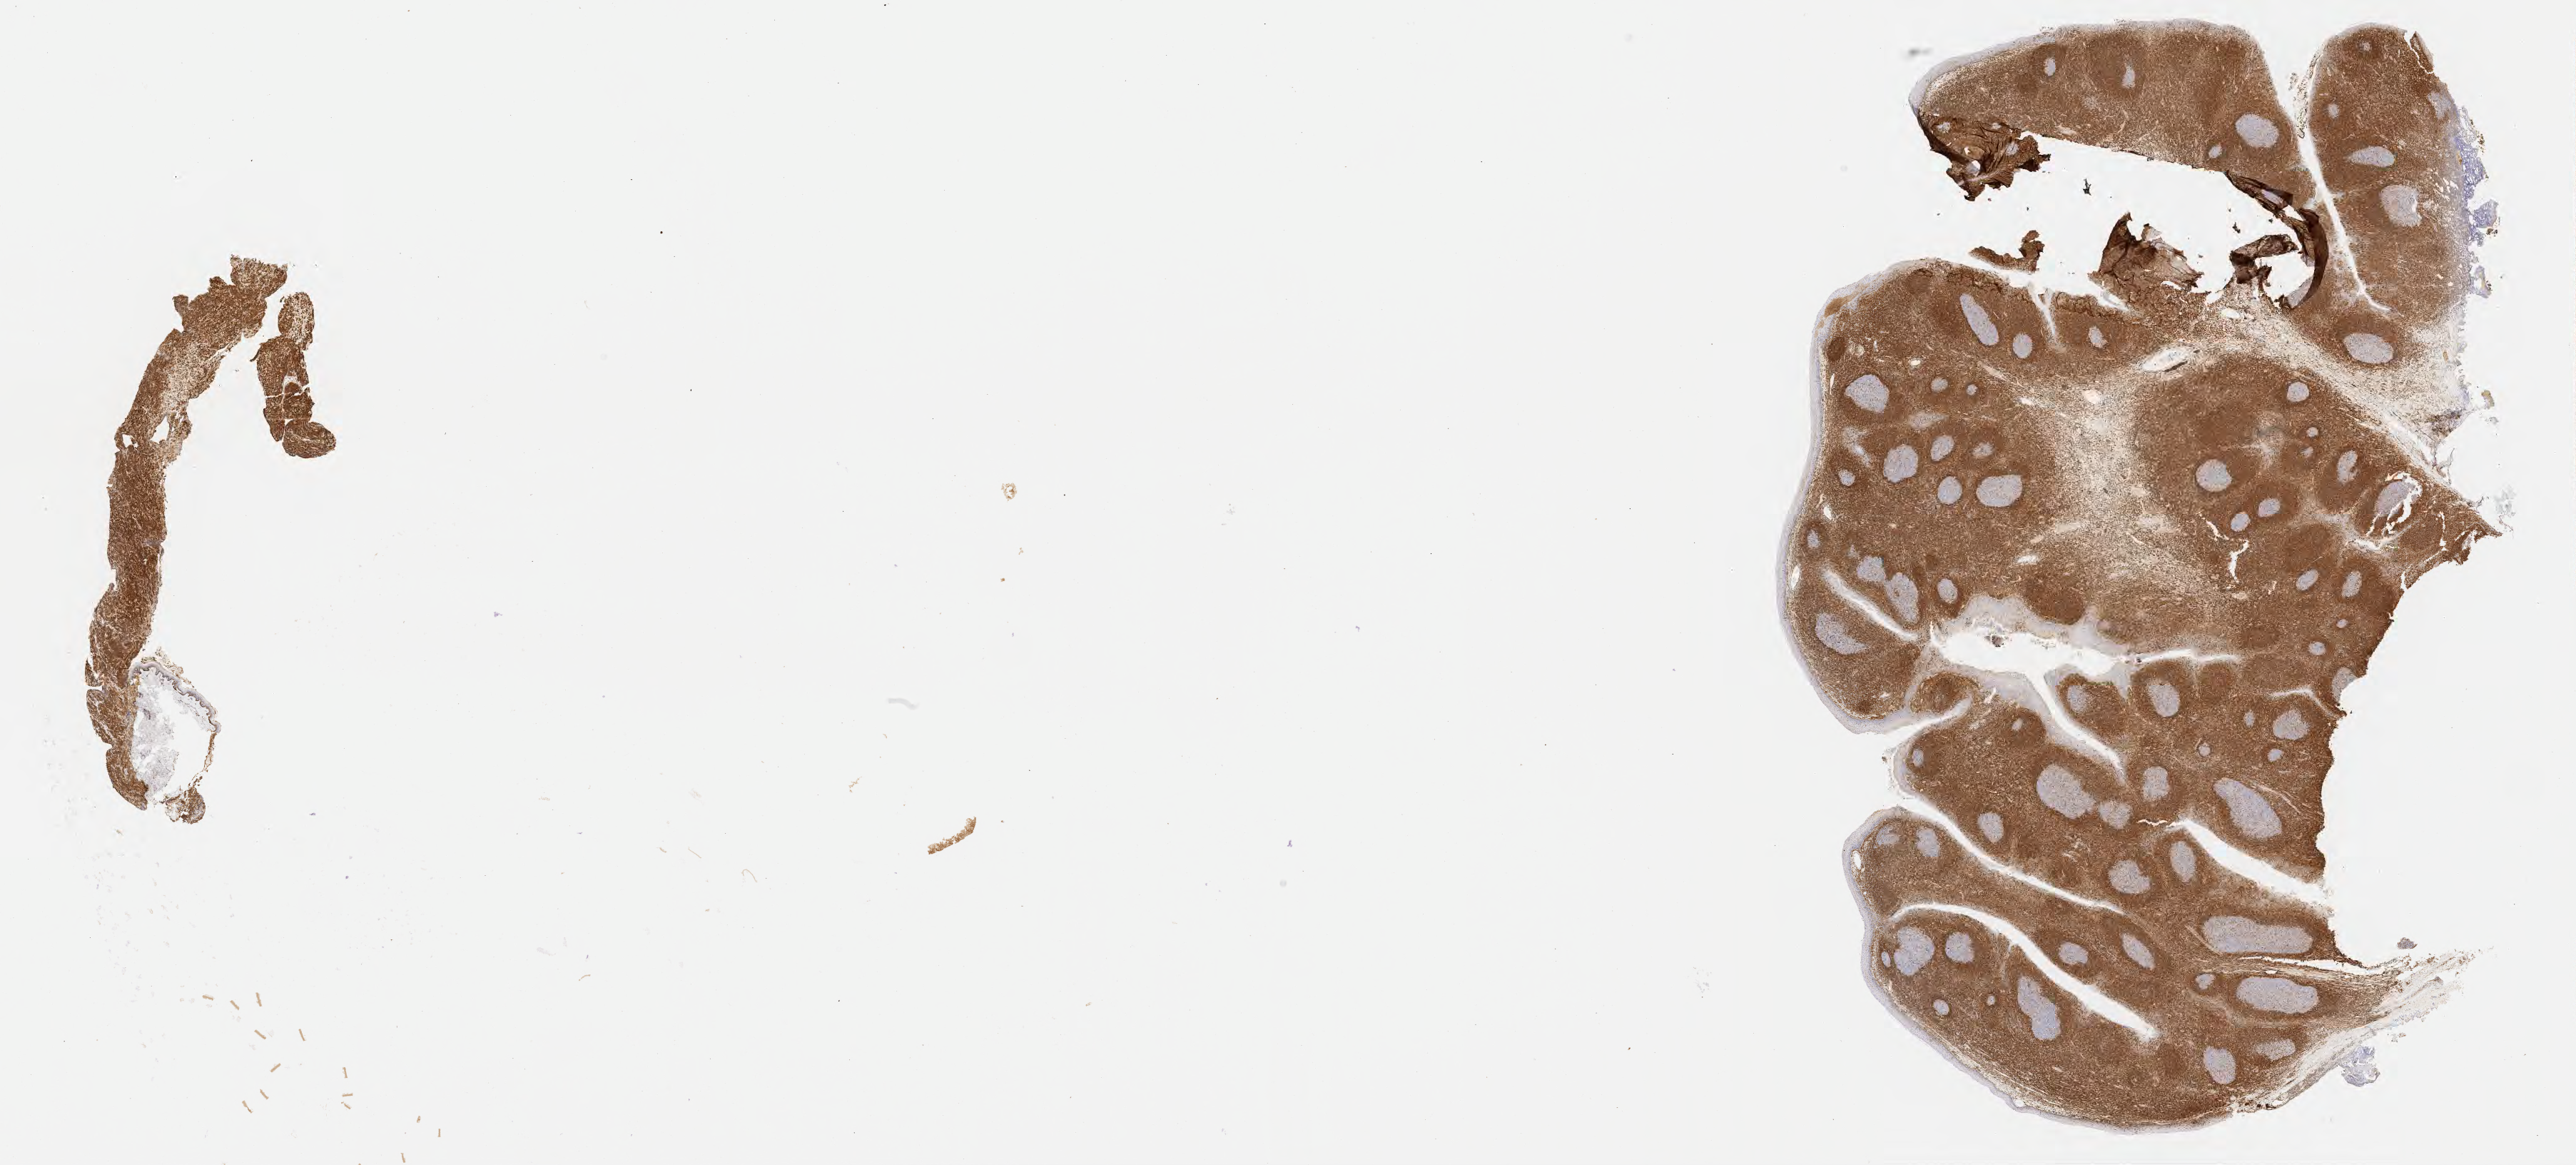
Whole-slide image, immunohistochemical stain for BCL2 — whole scanned area (about 29.2 x 13.2 mm) shown as a low-resolution overview, specimen: tumor tissue. Patient female; aged 43.
Diagnosis: Diffuse large B-cell lymphoma, NOS.